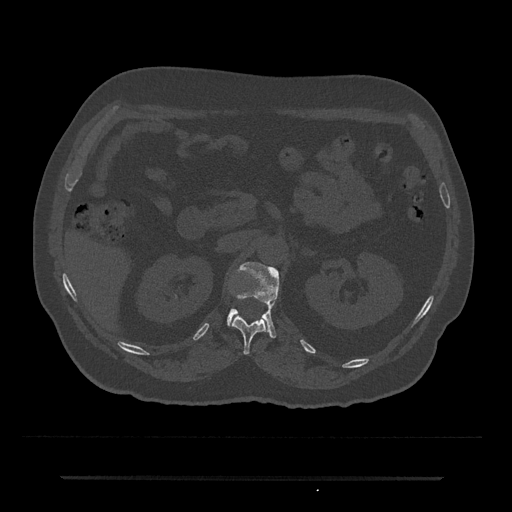
CT including the spine, one axial slice; slice 103 of 797 in the series (ordered by position); reconstruction kernel Br40s/3; 120 kVp; bone window (W 1800 / L 400 HU); 0.5 mm slice thickness; 512 × 512 image matrix. Male patient, age 69 years. Case-level facts recorded for this patient, not image findings: primary cancer: prostate.
Structures marked on this image (semi-automatically segmented with operator editing):
- L1 vertebra: bounding box [x1, y1, x2, y2] px = [227, 262, 279, 338]
- T12 vertebra: [232, 313, 267, 354]